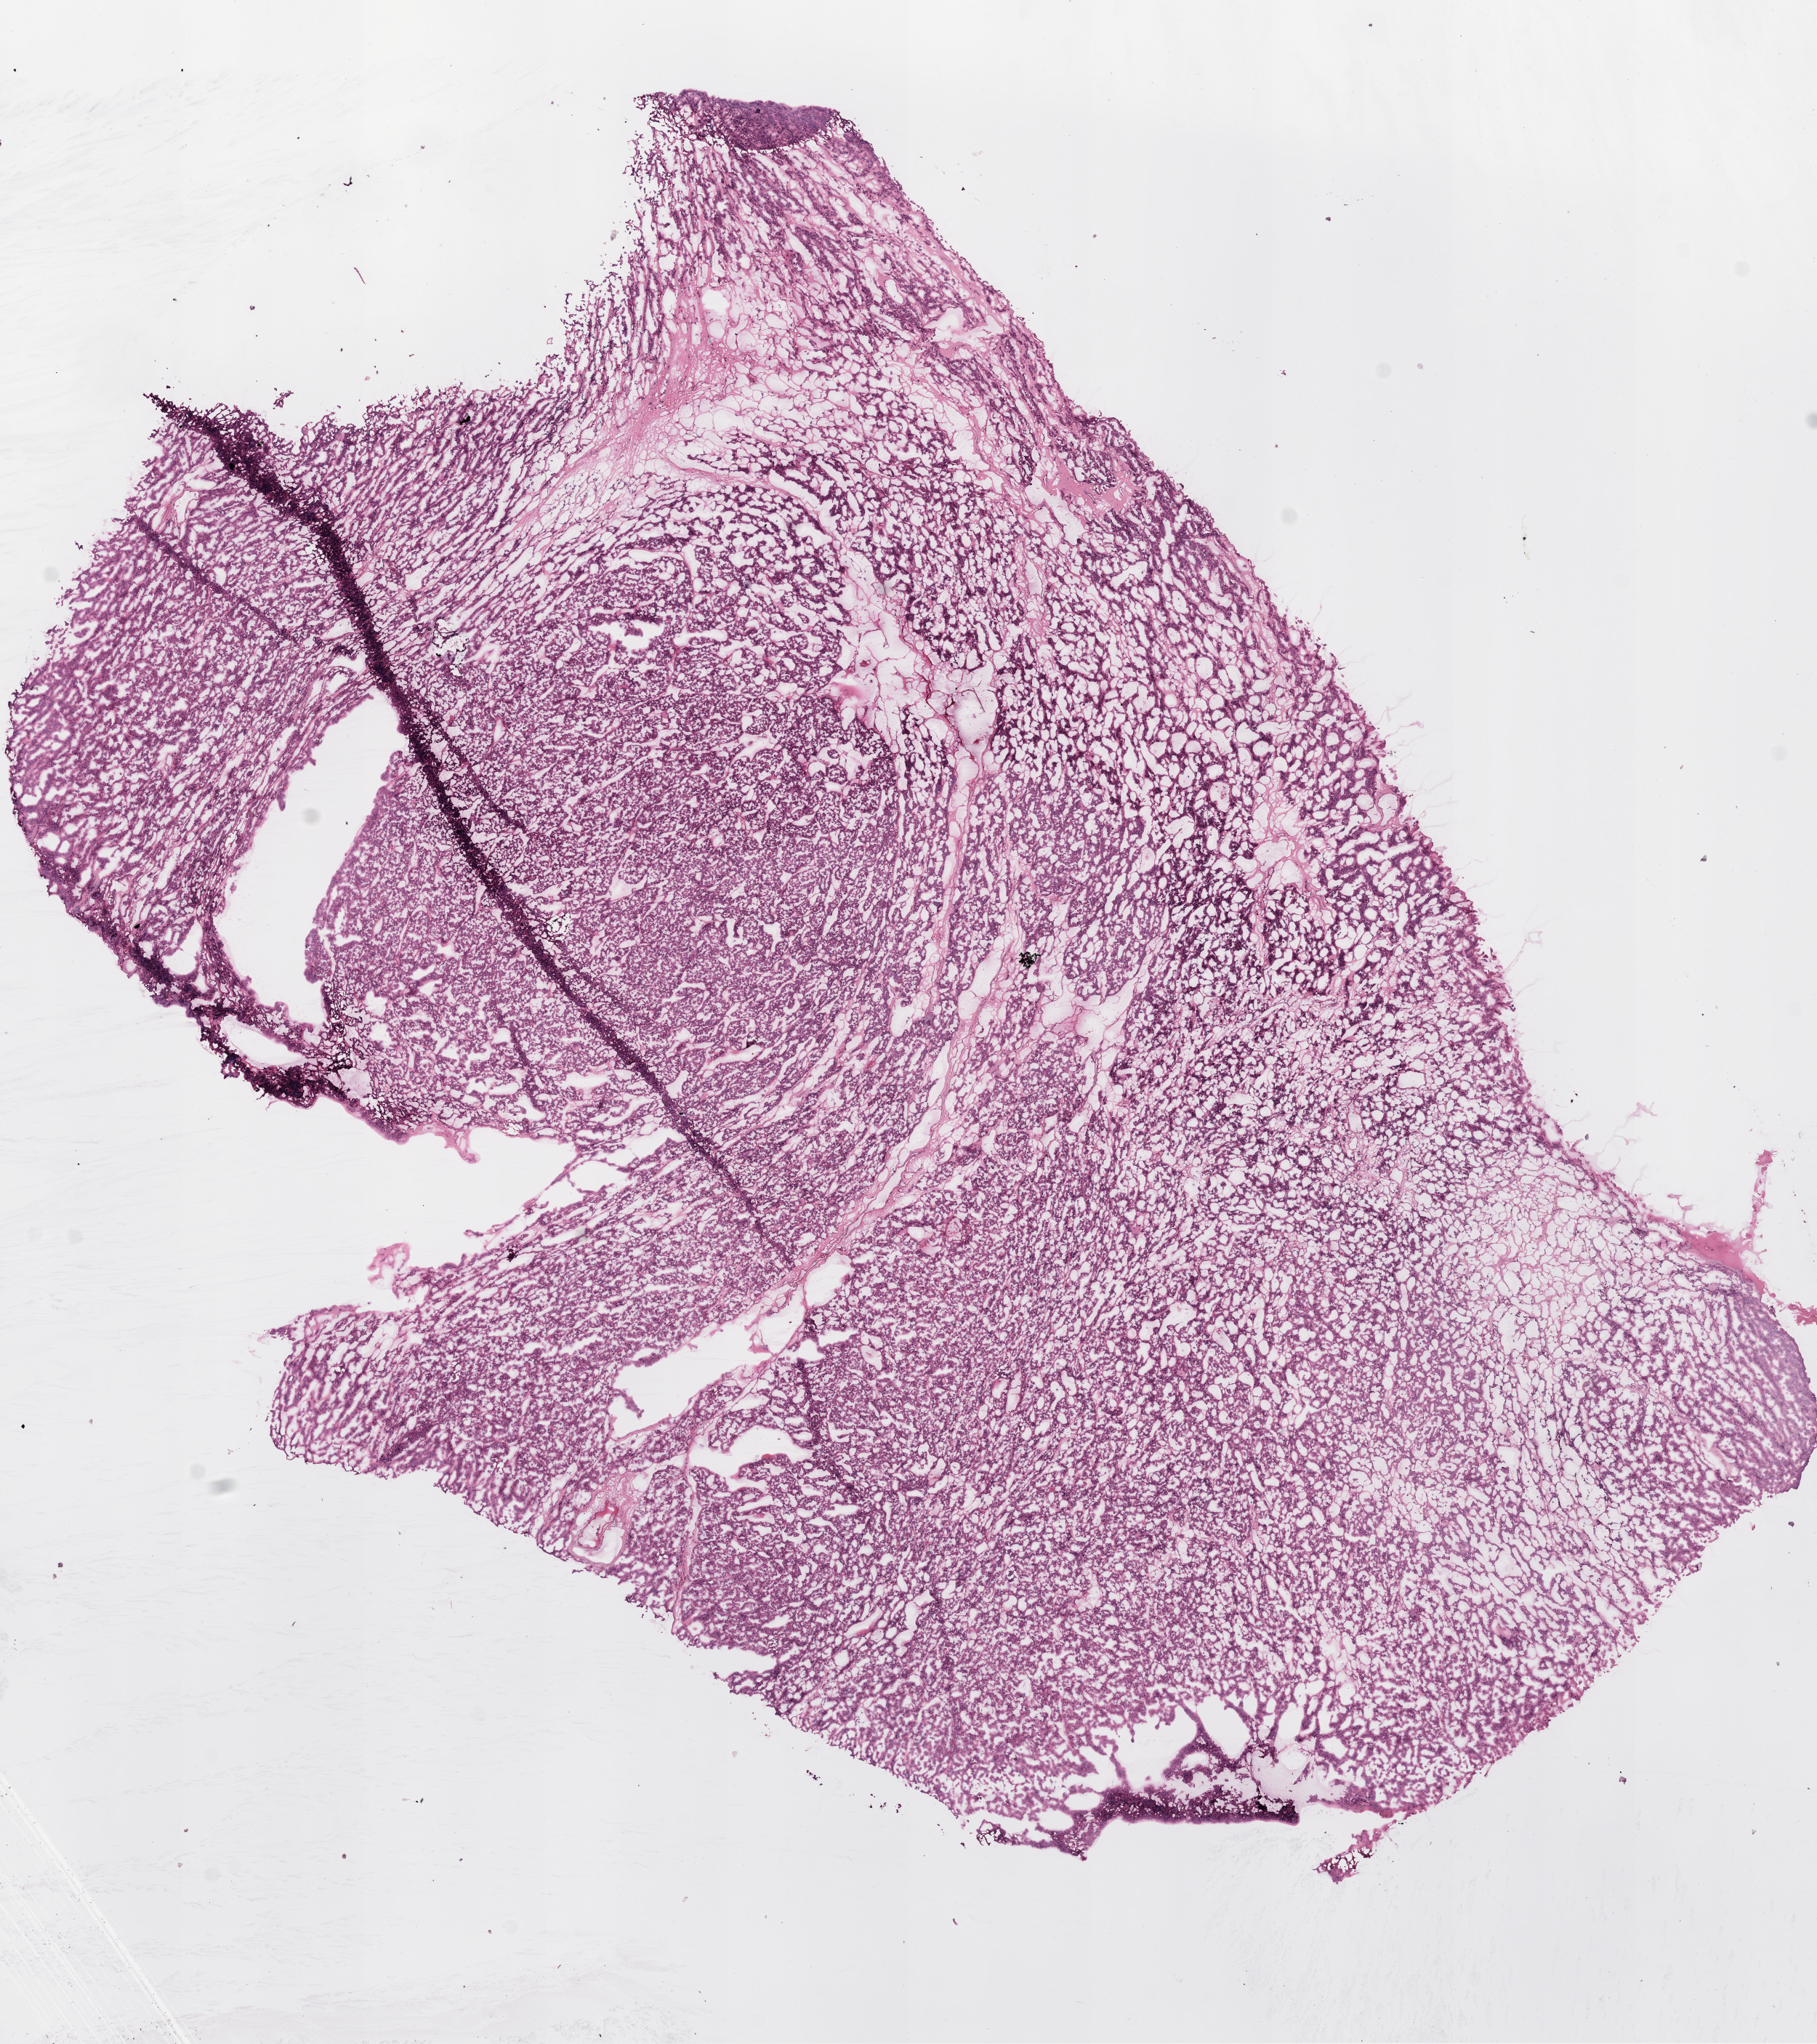
Hematoxylin and eosin (H&E) stained whole-slide image, shown as a low-resolution overview of the whole scanned area (about 10.0 x 11.3 mm, slide scanned at 20x); frozen section from the top of the tissue portion; primary tumour sample from the kidney. Male patient; age at initial diagnosis 65 years. Histologic grade: GX (grade cannot be assessed). Composition of this section per pathologist review: tumour cells 90%, tumour nuclei 85%, normal cells 0%, stromal cells 10%, necrosis 0%.
Lymph nodes positive (case pathology): 15 of 15 examined. TNM: T1a N0 M0. AJCC pathologic stage: I. Pathologic diagnosis: Clear cell adenocarcinoma, NOS.